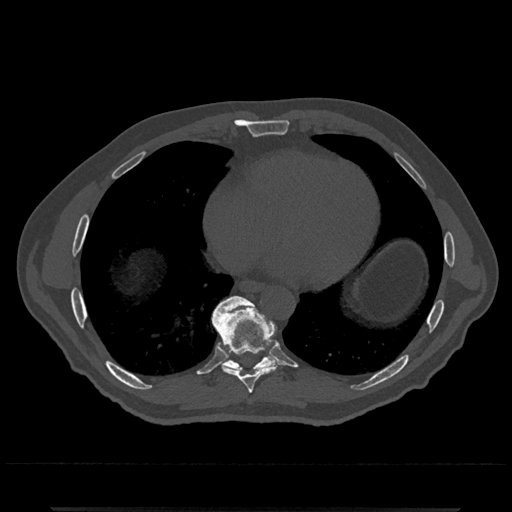
CT including the spine, one axial slice. Position 647 of 797 along the scan axis. Reconstruction kernel Br40s/3. 120 kVp. Bone window (W 1800 / L 400 HU). 0.5 mm slice thickness. 512 × 512 image matrix, field of view 393 × 393 mm. Male patient, age 67 years. Case-level facts recorded for this patient, not image findings: primary cancer: prostate.
Outlined on this slice (semi-automatically segmented with operator editing):
- T8 vertebra: bounding box (x1, y1, x2, y2) in pixels: (213, 306, 280, 394)
- T9 vertebra: (211, 296, 277, 371)